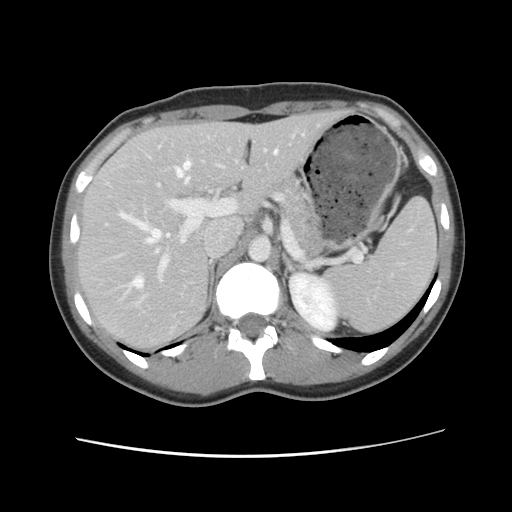
Contrast-enhanced abdominal CT, one axial slice. Slice 70 of 134 in the series (ordered by position). 120 kVp. Intravenous contrast given. Soft-tissue window (W 400 / L 40 HU). 2.5 mm slice thickness. 512 × 512 image matrix, field of view 339 × 339 mm. Female patient, age 33 years. From the clinical record (not read from this slice): diagnosis: colorectal cancer liver metastases, imaged before liver resection; multiple liver metastases: yes; largest metastasis: 4.5 cm; disease in both lobes: yes.
Structures marked on this image (outlined manually by an expert reader):
- hepatic veins: bounding box <121,150,278,297> (left, top, right, bottom; pixels)
- liver: <79,111,342,352>
- planned liver remnant (the part of the liver to remain after resection): <79,112,341,351>
- portal vein (with intrahepatic branches): <154,138,292,283>